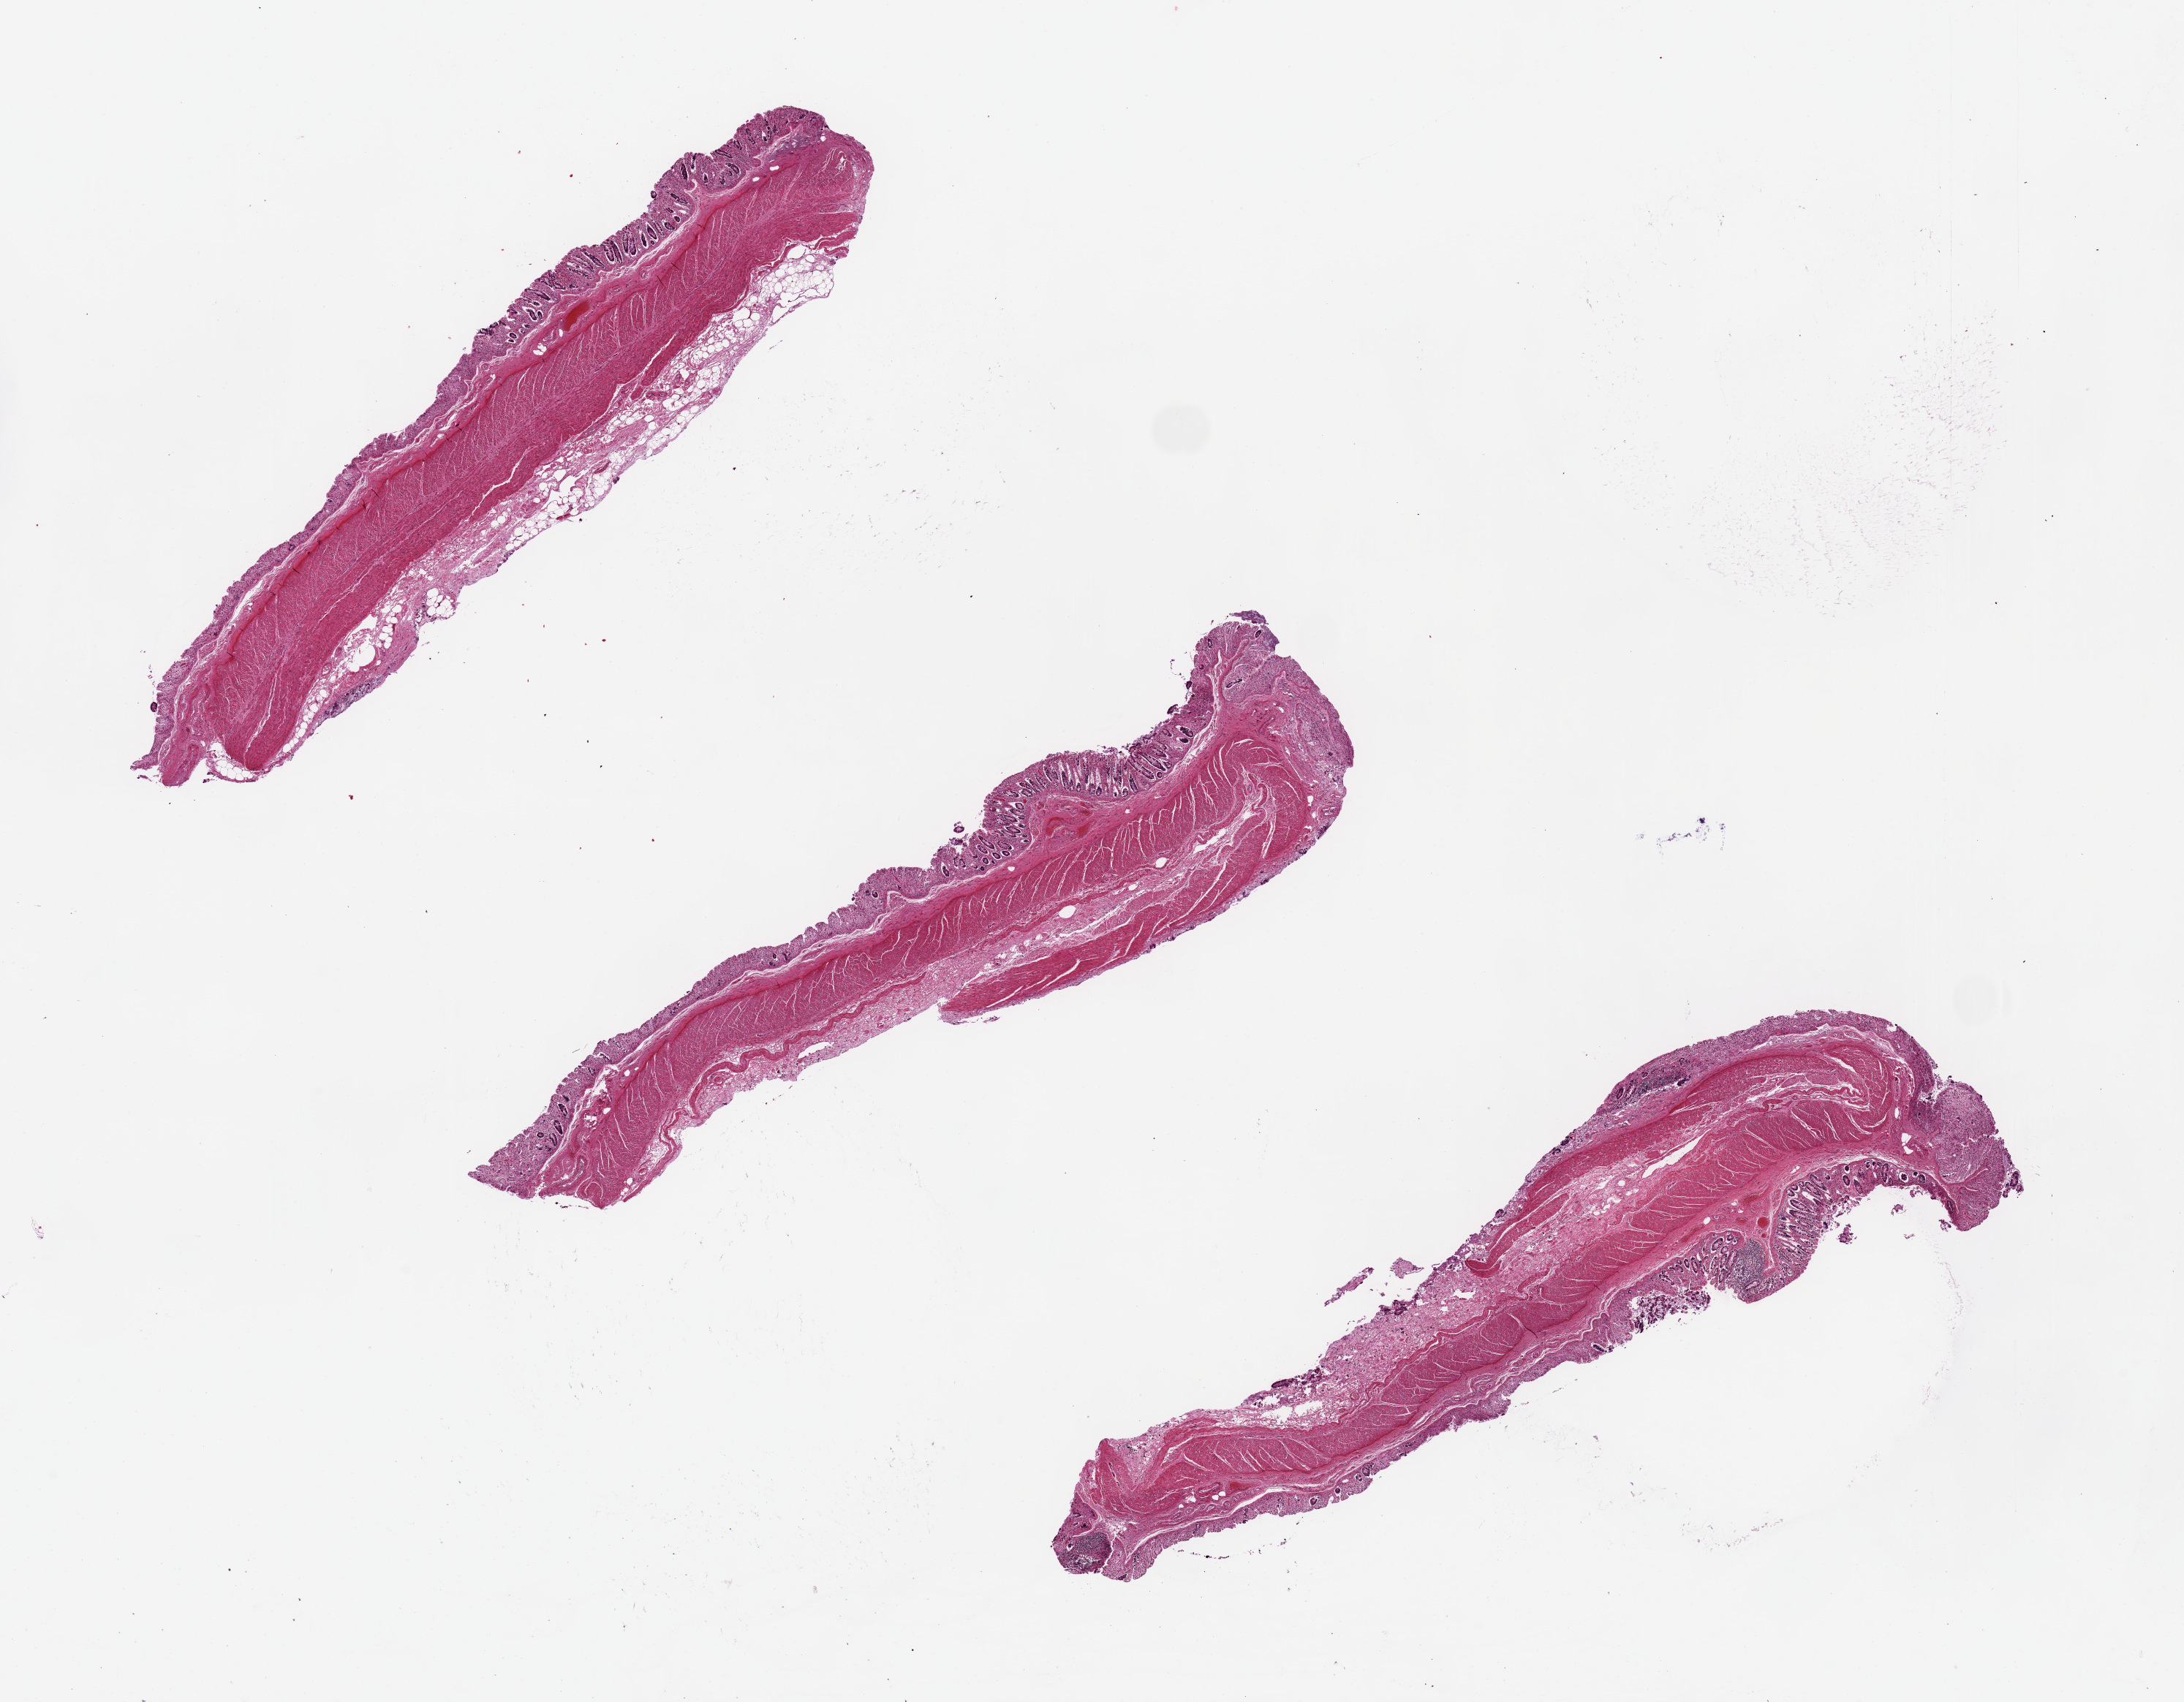
H&E whole-slide image — whole scanned area (about 23.6 x 18.4 mm) shown as a low-resolution overview; PAXgene-fixed, paraffin-embedded tissue; target tissue: transverse colon; tissue donor sample. Male donor.
* pathologist's review note for this sample: Glands ~90% autolyzed